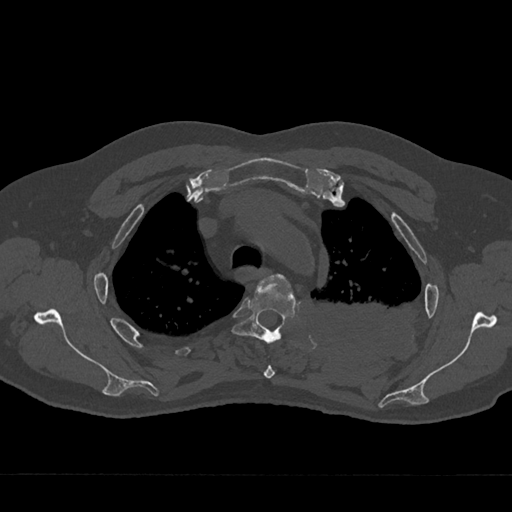
CT including the spine, one axial slice. Position 533 of 797 along the scan axis. Reconstruction kernel Br40s/3. 120 kVp. Bone window (W 1800 / L 400 HU). 0.5 mm slice thickness. 512 × 512 image matrix, field of view 377 × 377 mm. Patient: male, 75 years. Case-level facts recorded for this patient, not image findings: primary cancer: renal.
Annotated regions visible in this slice (semi-automatically segmented with operator editing):
- T3 vertebra: bounding box <263,275,291,379> (left, top, right, bottom; pixels)
- T4 vertebra: <231,278,296,344>